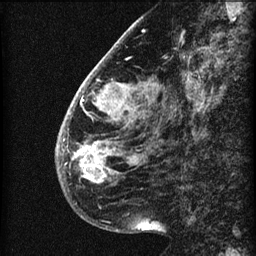
Breast MRI (dynamic contrast-enhanced), one sagittal slice. Position 19 of 60 along the scan axis. 3 images stored at this slice position (order not interpretable as contrast timing). 1.5 T. TE 4.2 ms, TR 22.7 ms. 2 mm slice thickness. 256 × 256 image matrix, field of view 180 × 180 mm. Patient: female, 48 years. Case-level facts recorded for this patient, not image findings: setting: breast cancer imaged before/during neoadjuvant chemotherapy; receptor status: triple-negative.
Outlined on this slice (semi-automatic segmentation, software-assisted and operator-edited):
- analysis volume of interest (the breast-tissue region the enhancement analysis was run in; not a lesion): bounding box <56,30,173,207> (left, top, right, bottom; pixels)
- tumour enhancement mask (voxels above the 90 % enhancement threshold inside the analysis volume of interest): <56,85,132,184>